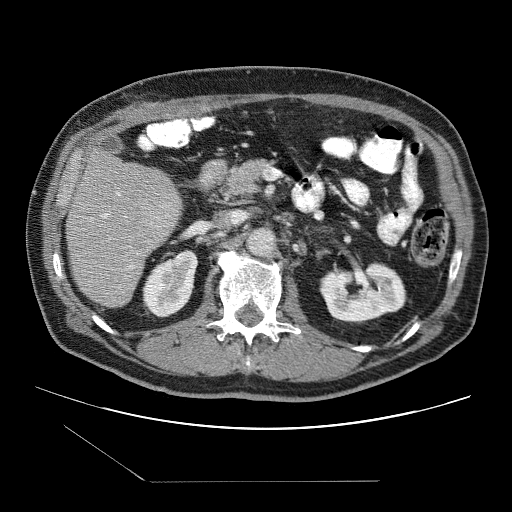
Contrast-enhanced abdominal CT (liver protocol), one axial slice. Slice 39 of 109 in the series (ordered by position). 120 kVp. One of 2 acquisitions stored at this slice position. Soft-tissue window (W 400 / L 40 HU). 2.5 mm slice thickness. 512 × 512 image matrix, field of view 400 × 400 mm. From the clinical record (not read from this slice): diagnosis: hepatocellular carcinoma (patient treated with transarterial chemoembolisation; whether this scan precedes or follows treatment is not stated here); TNM stage (as recorded): Stage-IIIB; Child-Pugh class: A; tumour differentiation: well differentiated.
Annotated regions visible in this slice (semi-automatic segmentation, software-assisted and operator-edited):
- liver parenchyma outside the tumour (the mass and vessels are separate outlines, so this box may not span the whole liver): bounding box (x1, y1, x2, y2) in pixels: (66, 148, 182, 306)
- liver vessels: (92, 192, 152, 289)